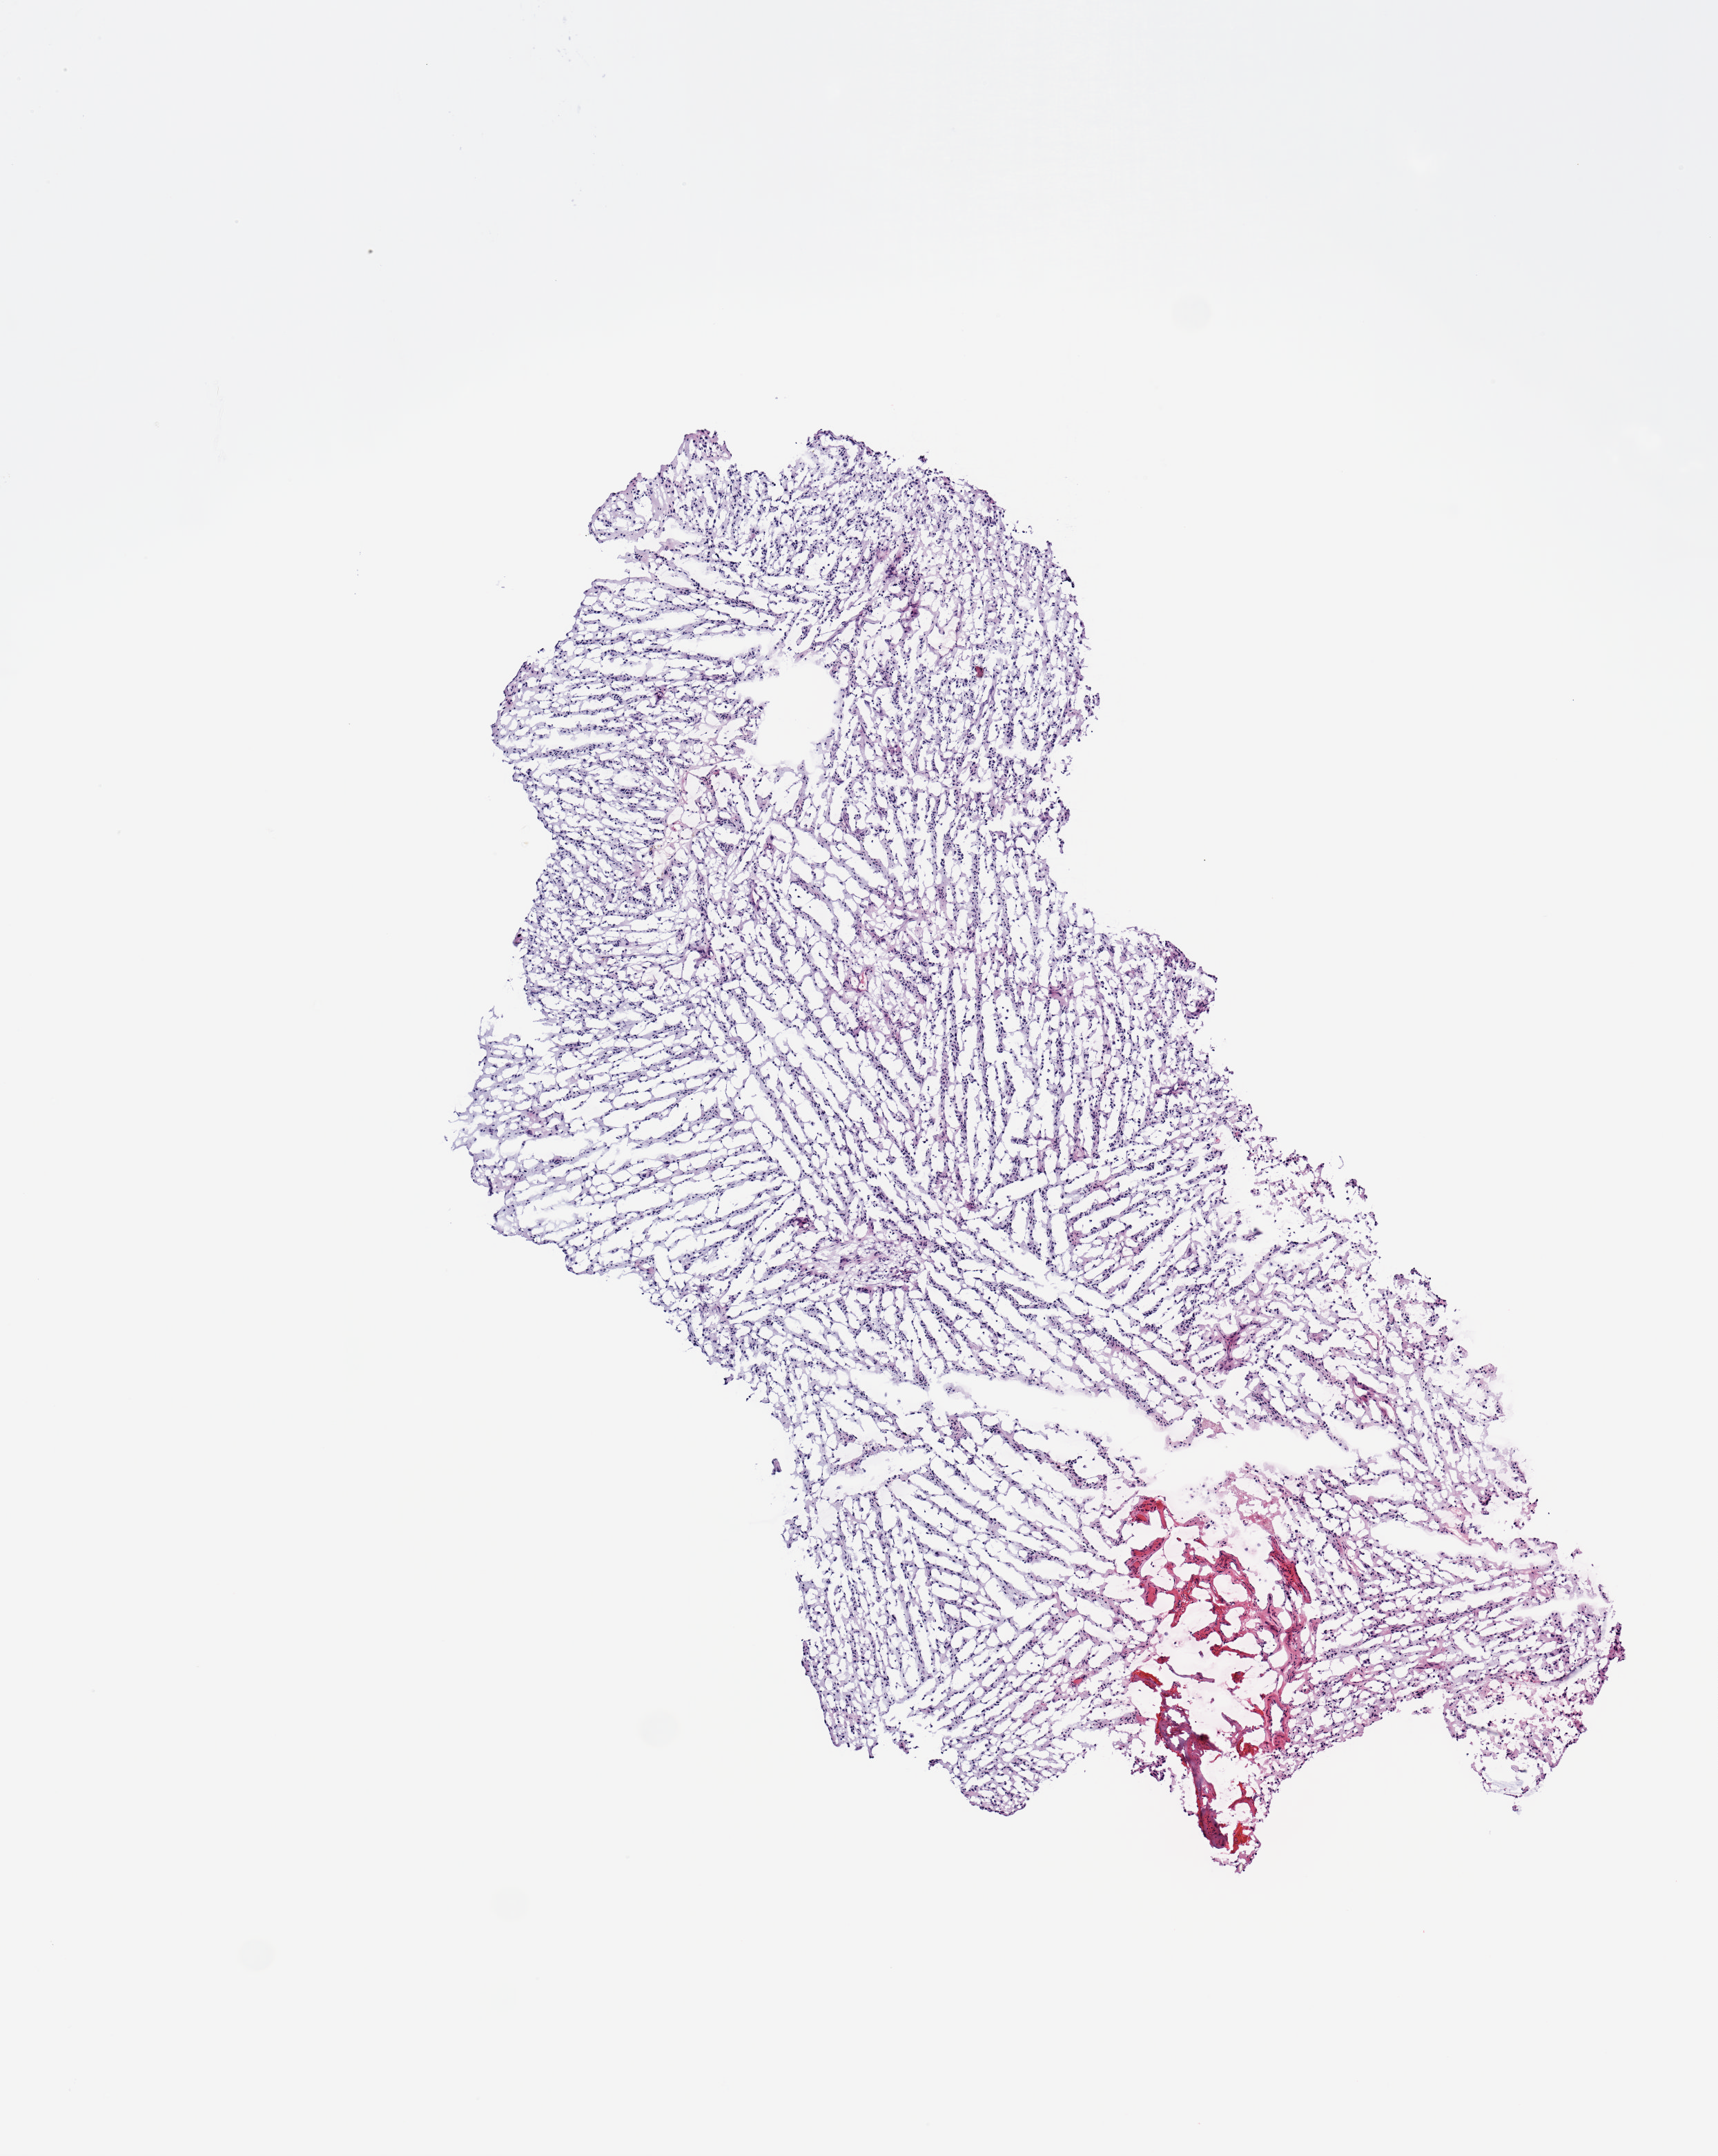
Whole-slide histology image, Hematoxylin and eosin (H&E) stained — low-resolution overview of the scanned area, about 4.9 x 6.2 mm (slide scanned at 20x); brain, tumour tissue. Male, 82 y/o.
Patient diagnosis (cohort enrolment): glioblastoma multiforme (brain). Primary tumour site (as recorded): temporal lobe.